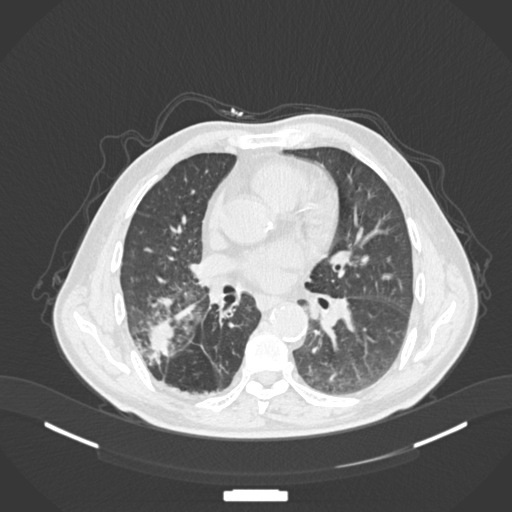
Chest CT, one axial slice. Slice 80 of 201 in the series (ordered by position). 120 kVp. Lung window (W 1500 / L -600 HU). 1 mm slice thickness. 512 × 512 image matrix, field of view 400 × 400 mm. Male patient, age 72 years. From the clinical record (not read from this slice): clinical TNM (as recorded): T3 N2 M0.
Annotated regions visible in this slice (bounding box drawn by a radiologist):
- lung tumour (recorded histology: adenocarcinoma): bounding box (x1, y1, x2, y2) in pixels: (146, 317, 179, 360)